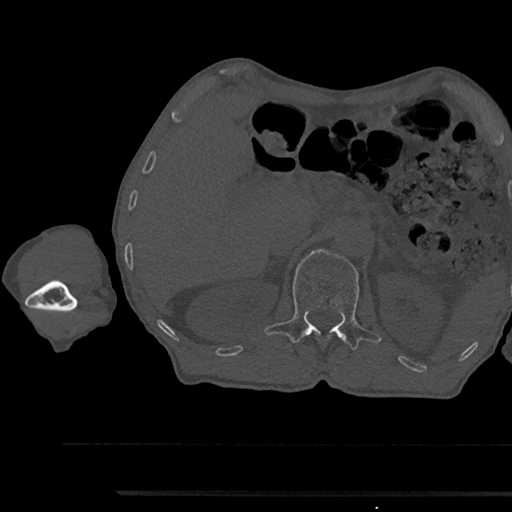
CT including the spine, one axial slice. Slice 650 of 797 in the series (ordered by position). Reconstruction kernel Br40s/3. 120 kVp. Bone window (W 1800 / L 400 HU). 512 × 512 image matrix, field of view 367 × 367 mm. Male patient, age 79 years. Case-level facts recorded for this patient, not image findings: primary cancer: prostate.
Annotated regions visible in this slice (semi-automatically segmented with operator editing):
- L1 vertebra: bounding box <264,248,381,350> (left, top, right, bottom; pixels)